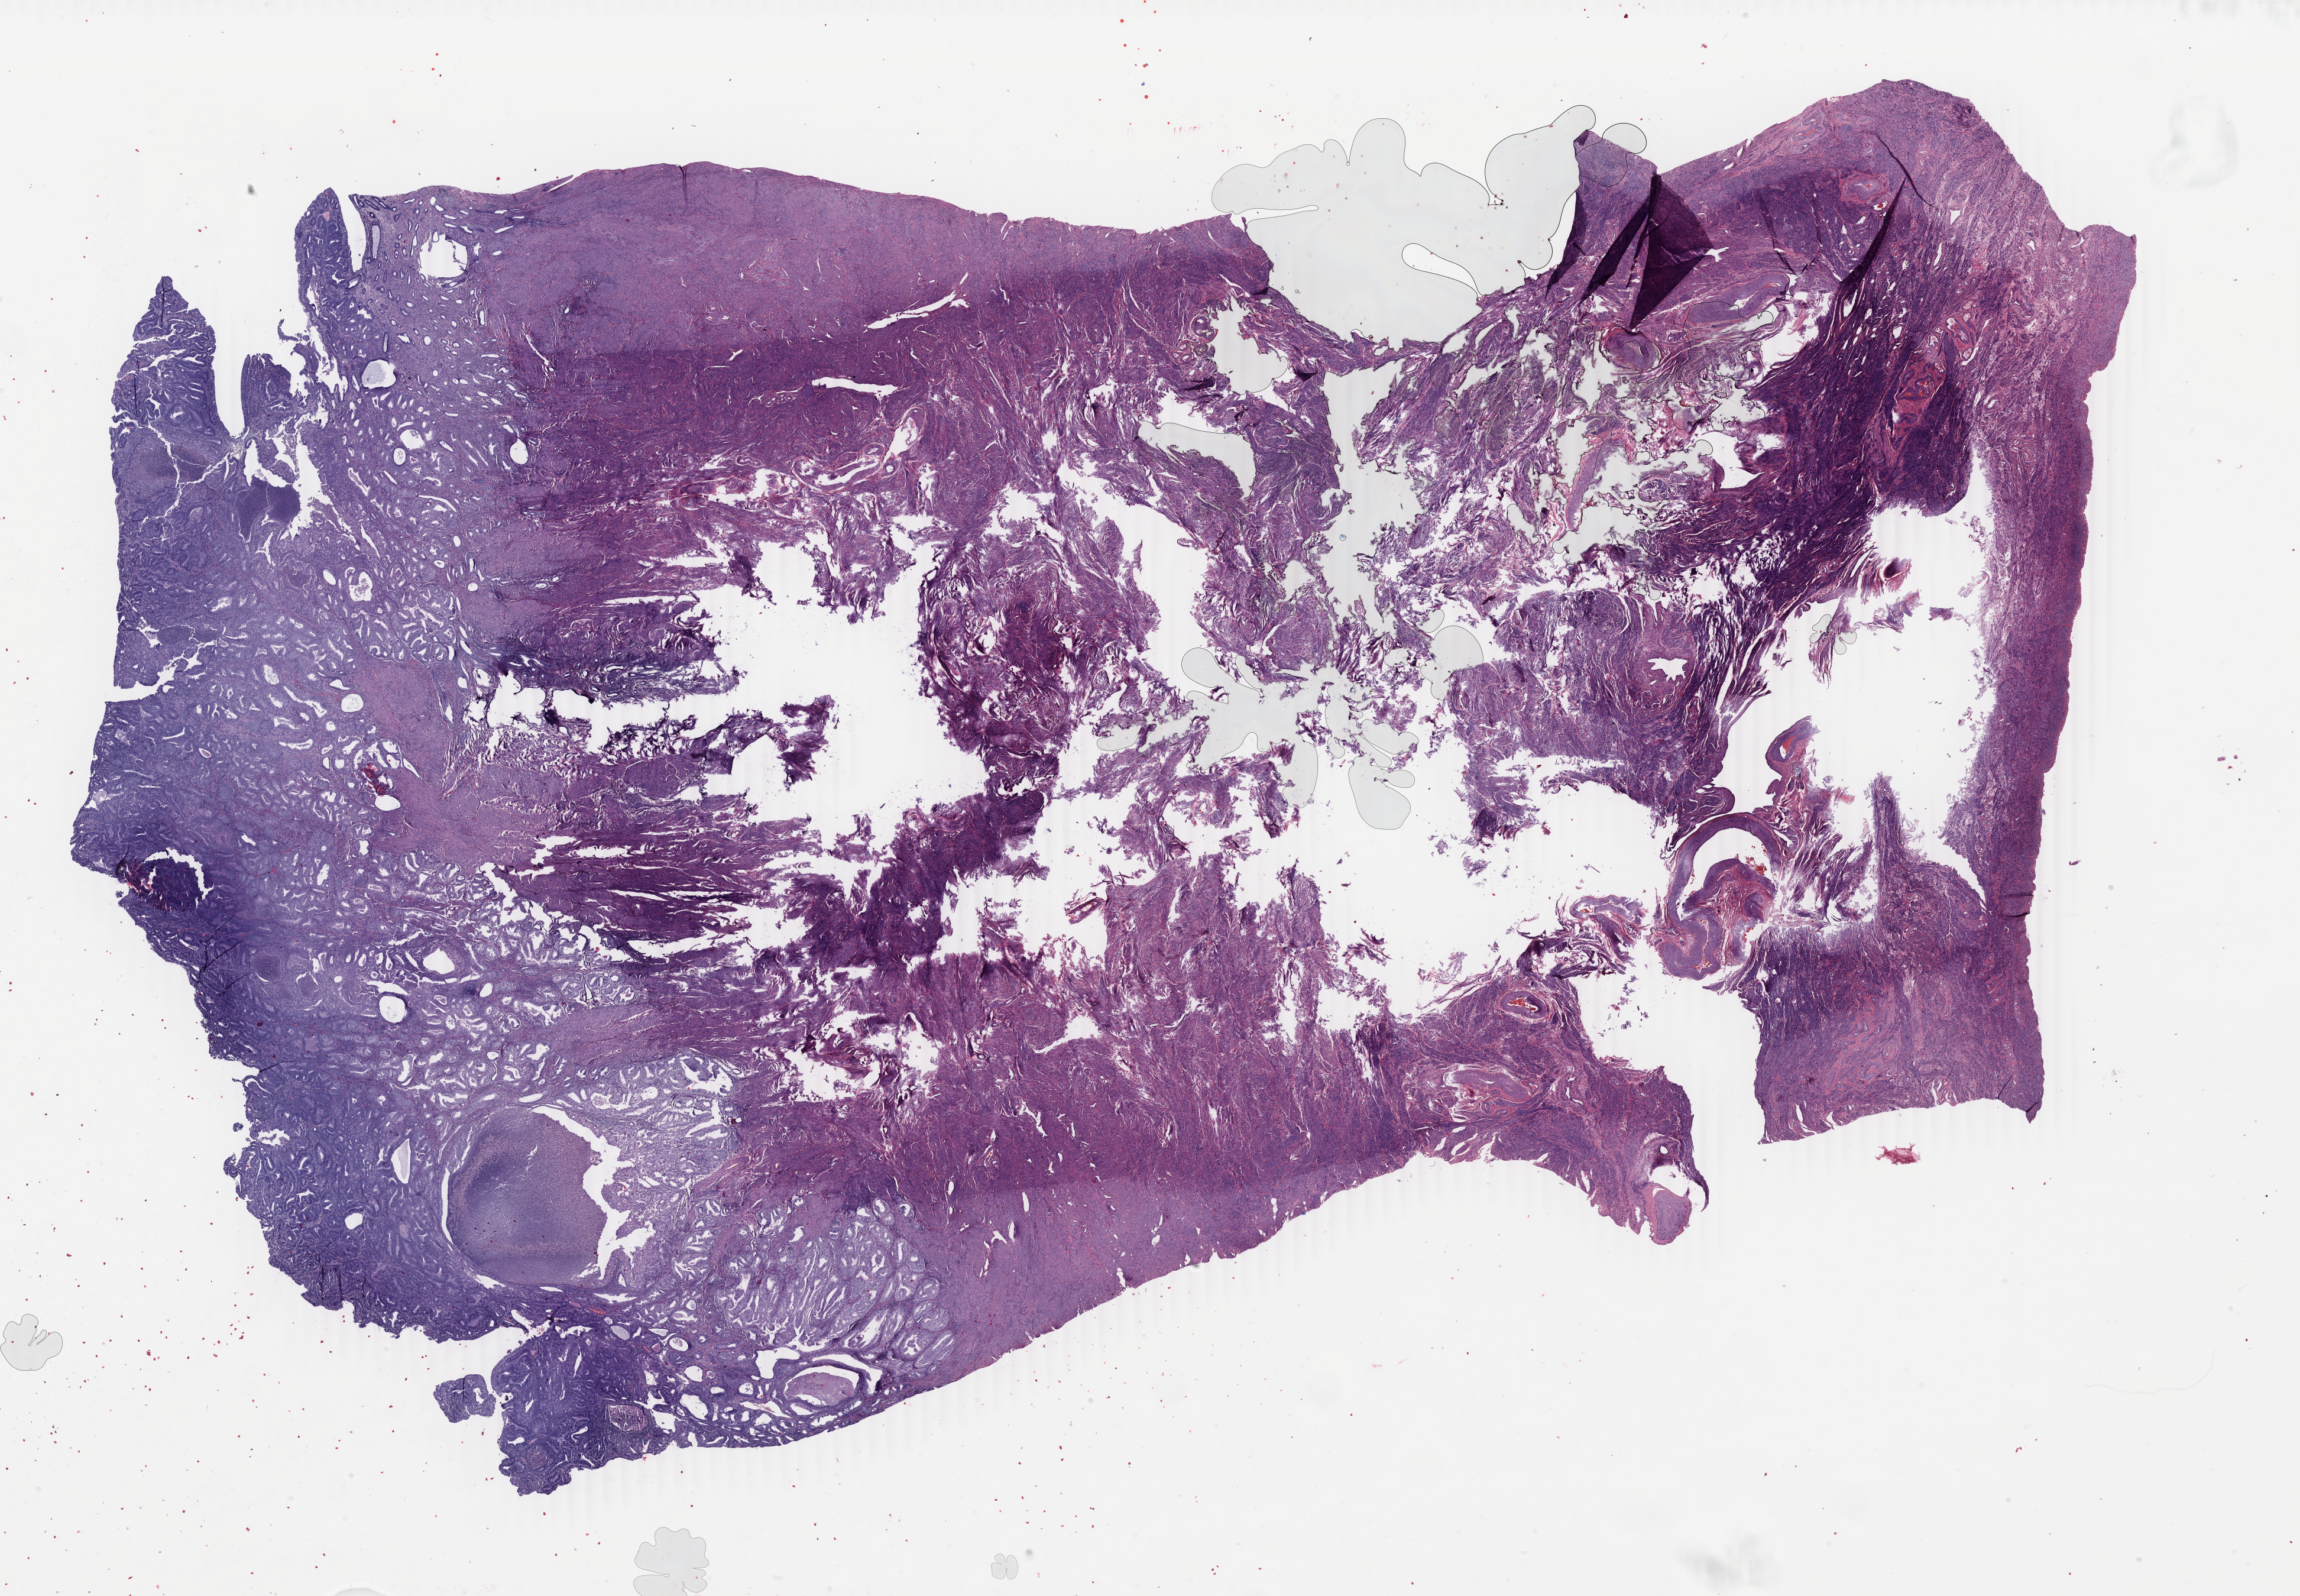
Whole-slide histology image, H&E-stained — a low-resolution overview of the entire scanned area, about 30.9 x 21.5 mm (acquisition: 40x scan). Formalin-fixed paraffin-embedded (FFPE) diagnostic section. Primary tumour sample from the uterus. Female, age 53 years at initial diagnosis. Histologic grade: G1 (well differentiated).
- diagnosis: Endometrioid adenocarcinoma, NOS (endometrium)
- FIGO stage: IA